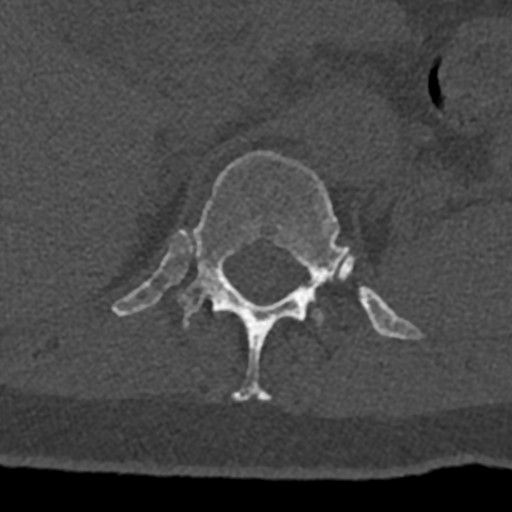
CT including the spine, one axial slice; position 492 of 797 along the scan axis; bone window (W 1800 / L 400 HU); 512 × 512 image matrix, field of view 160 × 160 mm. Patient: male, 74 years. Case-level facts recorded for this patient, not image findings: primary cancer: renal; vertebrae with lytic lesions (as recorded): T10, L1, L2, L3, L4, L5.
Annotated regions visible in this slice (semi-automatically segmented with operator editing):
- L1 vertebra: bounding box (x1, y1, x2, y2) in pixels: (312, 300, 323, 324)
- T12 vertebra: (112, 151, 422, 401)